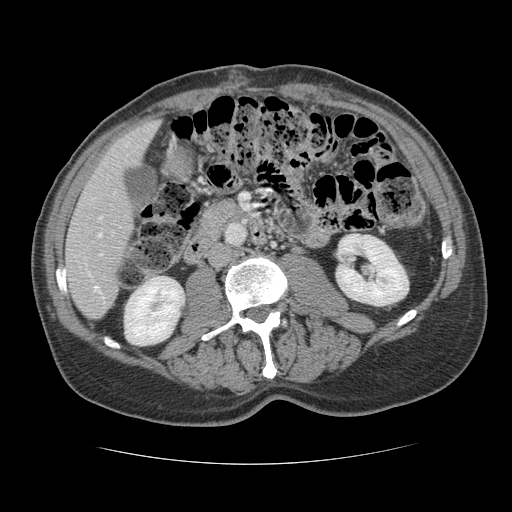
Contrast-enhanced abdominal CT, one axial slice; position 44 of 134 along the scan axis; 120 kVp; intravenous contrast given; soft-tissue window (W 400 / L 40 HU); 512 × 512 image matrix, field of view 377 × 377 mm. Male patient, age 68 years. From the clinical record (not read from this slice): diagnosis: colorectal cancer liver metastases, imaged before liver resection; multiple liver metastases: yes; largest metastasis: 2.2 cm; disease in both lobes: no.
Annotated regions visible in this slice (expert manual segmentation):
- hepatic veins: bounding box (x1, y1, x2, y2) in pixels: (98, 217, 102, 237)
- liver: (66, 120, 158, 319)
- planned liver remnant (the part of the liver to remain after resection): (66, 121, 158, 319)
- portal vein (with intrahepatic branches): (94, 254, 102, 290)